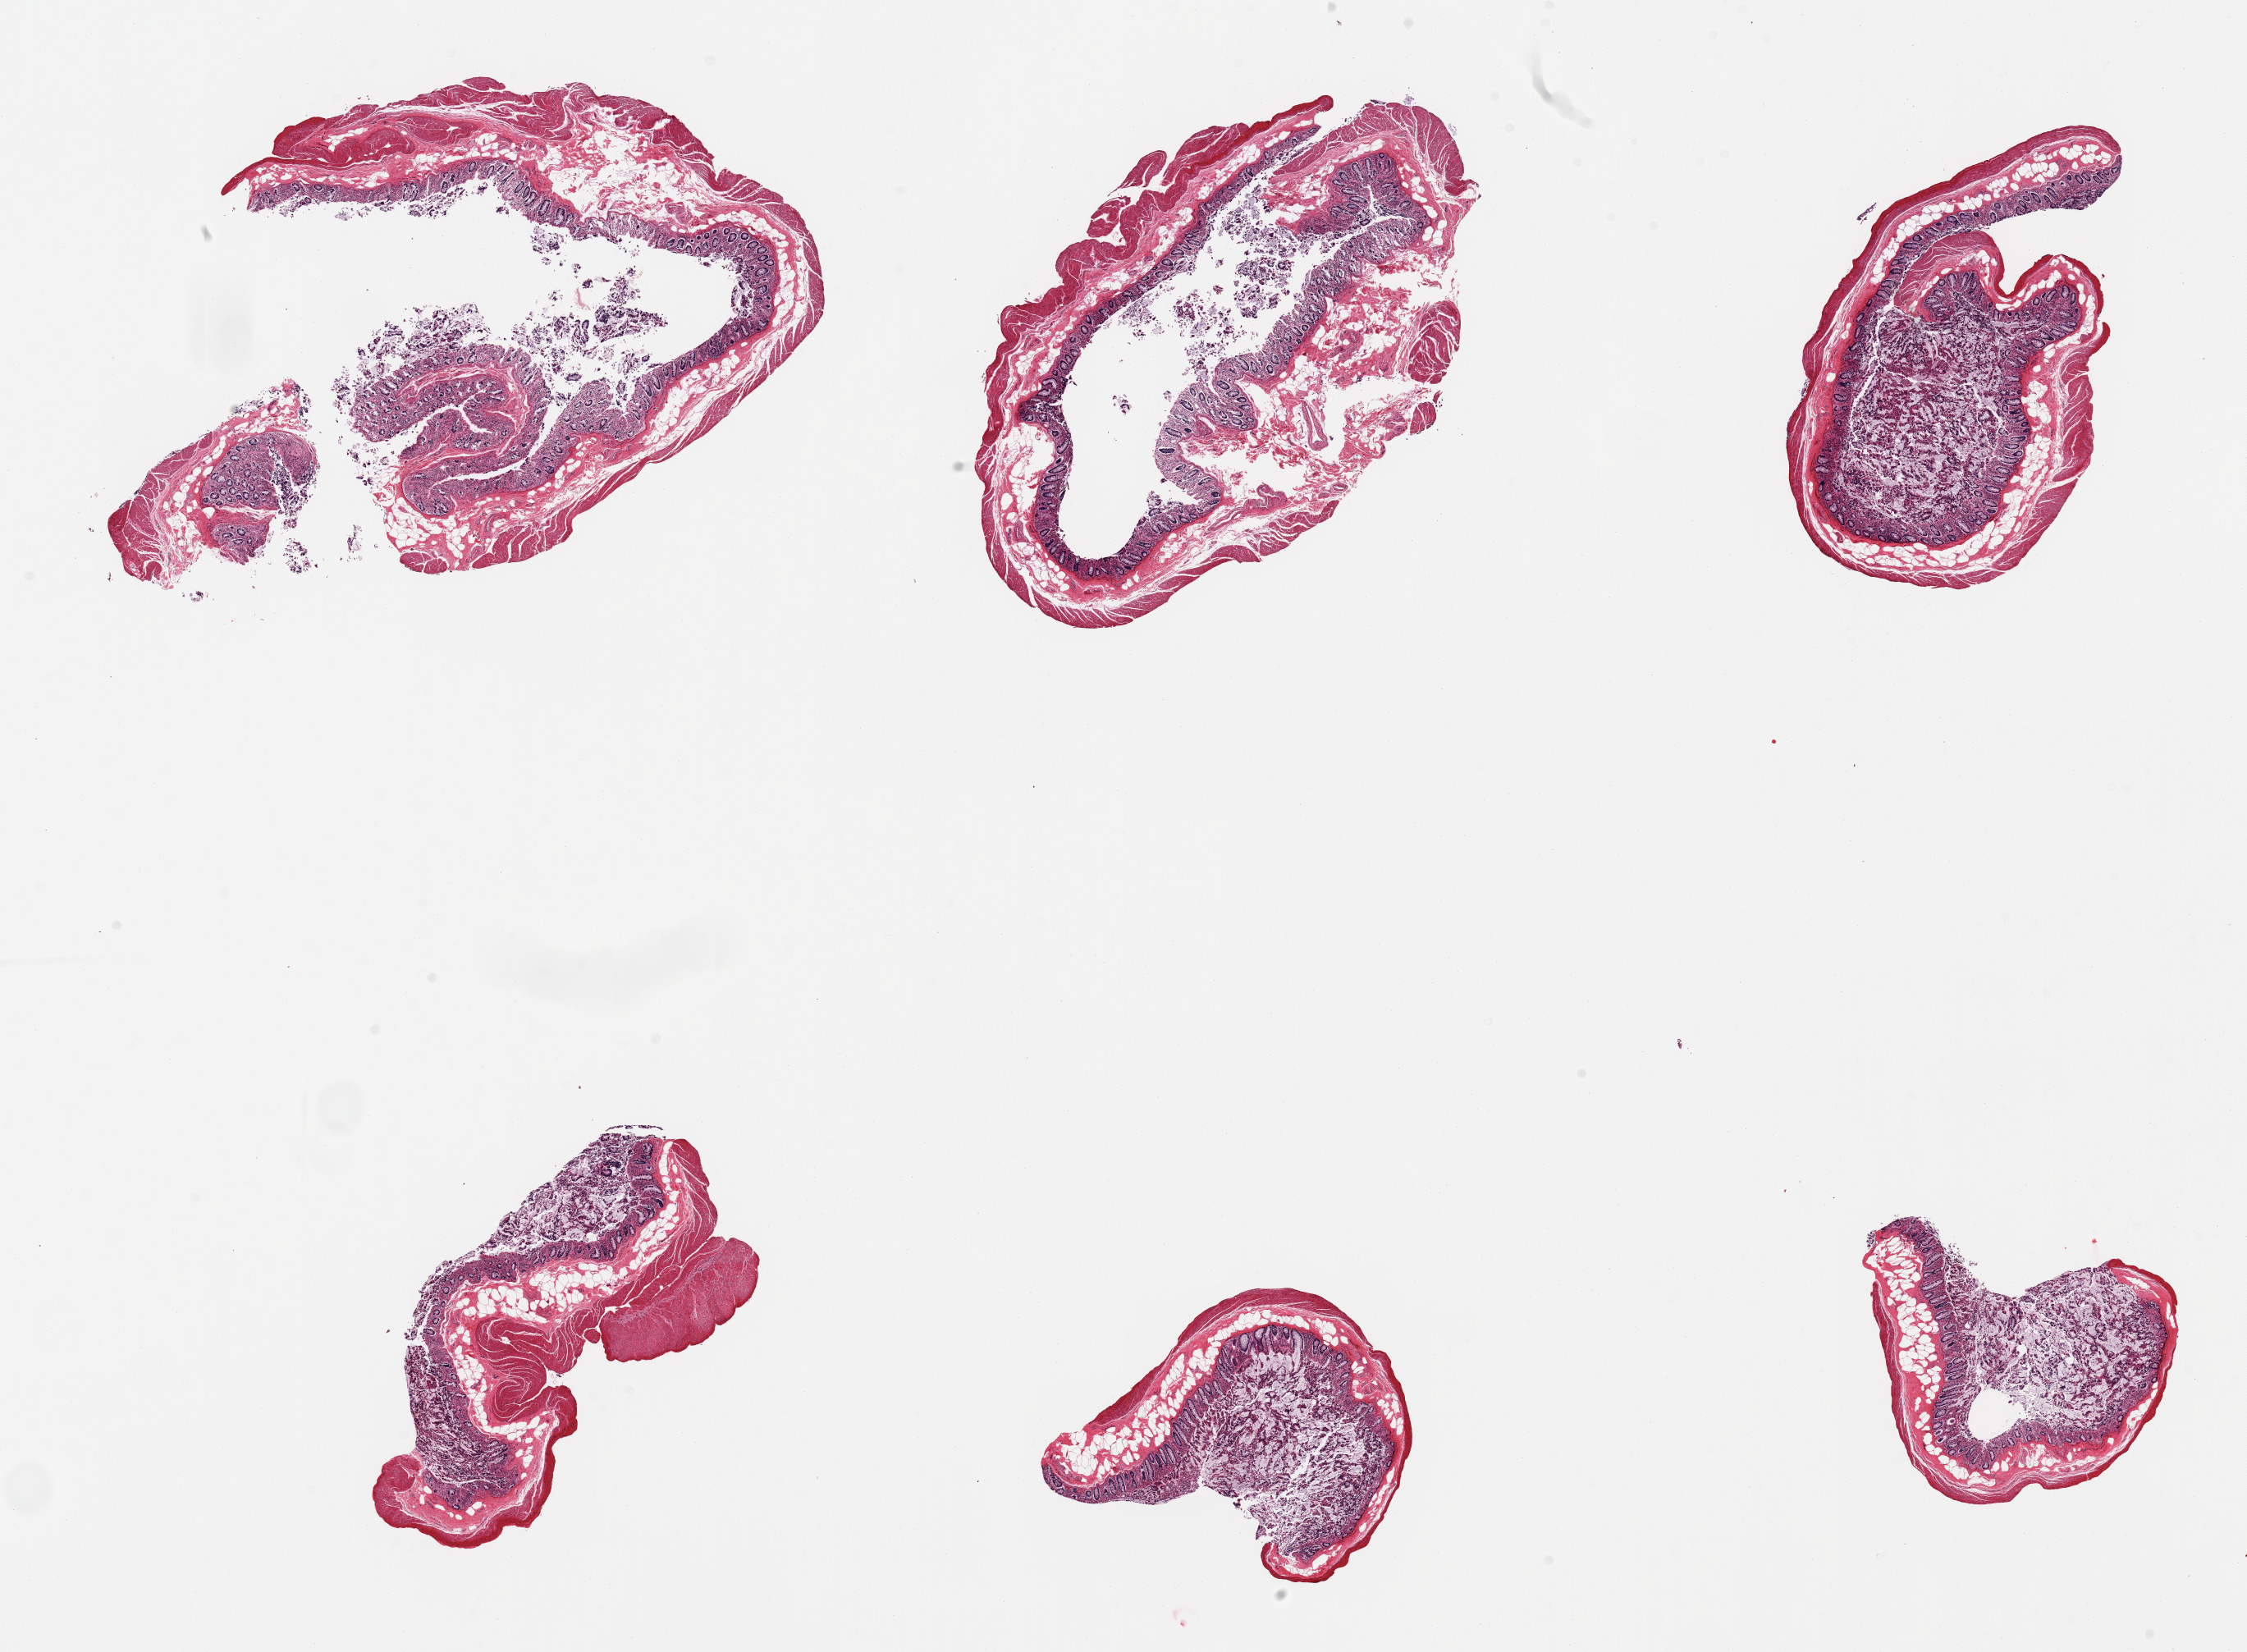
Haematoxylin and eosin whole-slide image, low-resolution overview of the scanned area, about 21.7 x 15.9 mm (acquisition: 20x scan); PAXgene-fixed paraffin-embedded (PFPE) section; section of transverse colon (target tissue); donor tissue sample.
Reviewer comment on this tissue sample: 6 pieces; minimal muscularis propria.